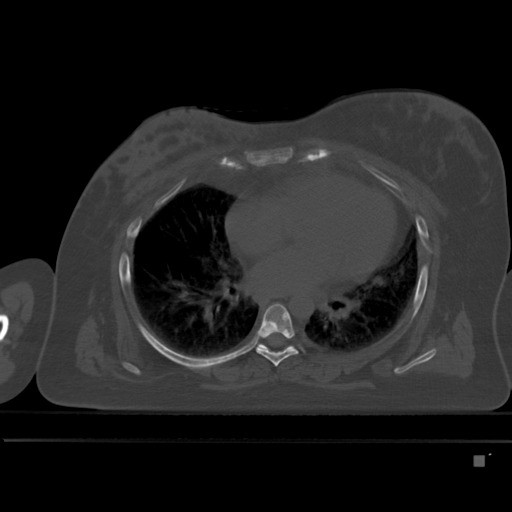
CT including the spine, one axial slice. Slice 303 of 495 in the series (ordered by position). Bone window (W 1800 / L 400 HU). 1.5 mm slice thickness. 512 × 512 image matrix. Female patient, age 33 years. From the clinical record (not read from this slice): primary cancer: breast; vertebrae with lytic lesions (as recorded): T1.
Outlined on this slice (semi-automatic segmentation, software-assisted and operator-edited):
- T6 vertebra: bounding box [x1, y1, x2, y2] px = [256, 303, 298, 366]
- T7 vertebra: [257, 343, 295, 350]